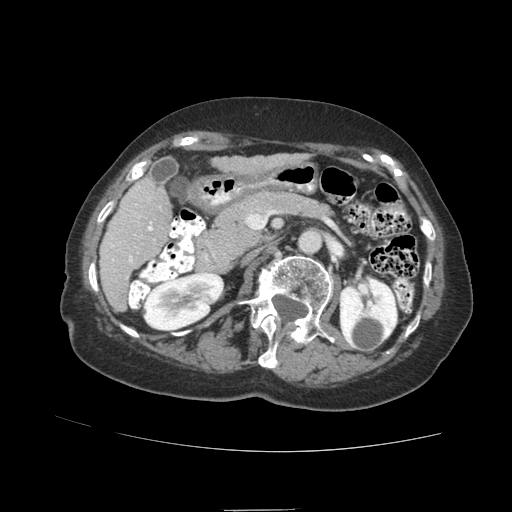
Contrast-enhanced abdominal CT (liver protocol), one axial slice. Slice 32 of 89 in the series (ordered by position). 140 kVp. Soft-tissue window (W 400 / L 40 HU). 2.5 mm slice thickness. 512 × 512 image matrix, field of view 360 × 360 mm. From the clinical record (not read from this slice): diagnosis: hepatocellular carcinoma (patient treated with transarterial chemoembolisation; whether this scan precedes or follows treatment is not stated here); TNM stage (as recorded): Stage-II; Child-Pugh class: A; tumour size: 4 cm.
Annotated regions visible in this slice (semi-automatically segmented with operator editing):
- liver parenchyma outside the tumour (the mass and vessels are separate outlines, so this box may not span the whole liver): bounding box (x1, y1, x2, y2) in pixels: (100, 154, 282, 310)
- liver vessels: (109, 221, 153, 278)